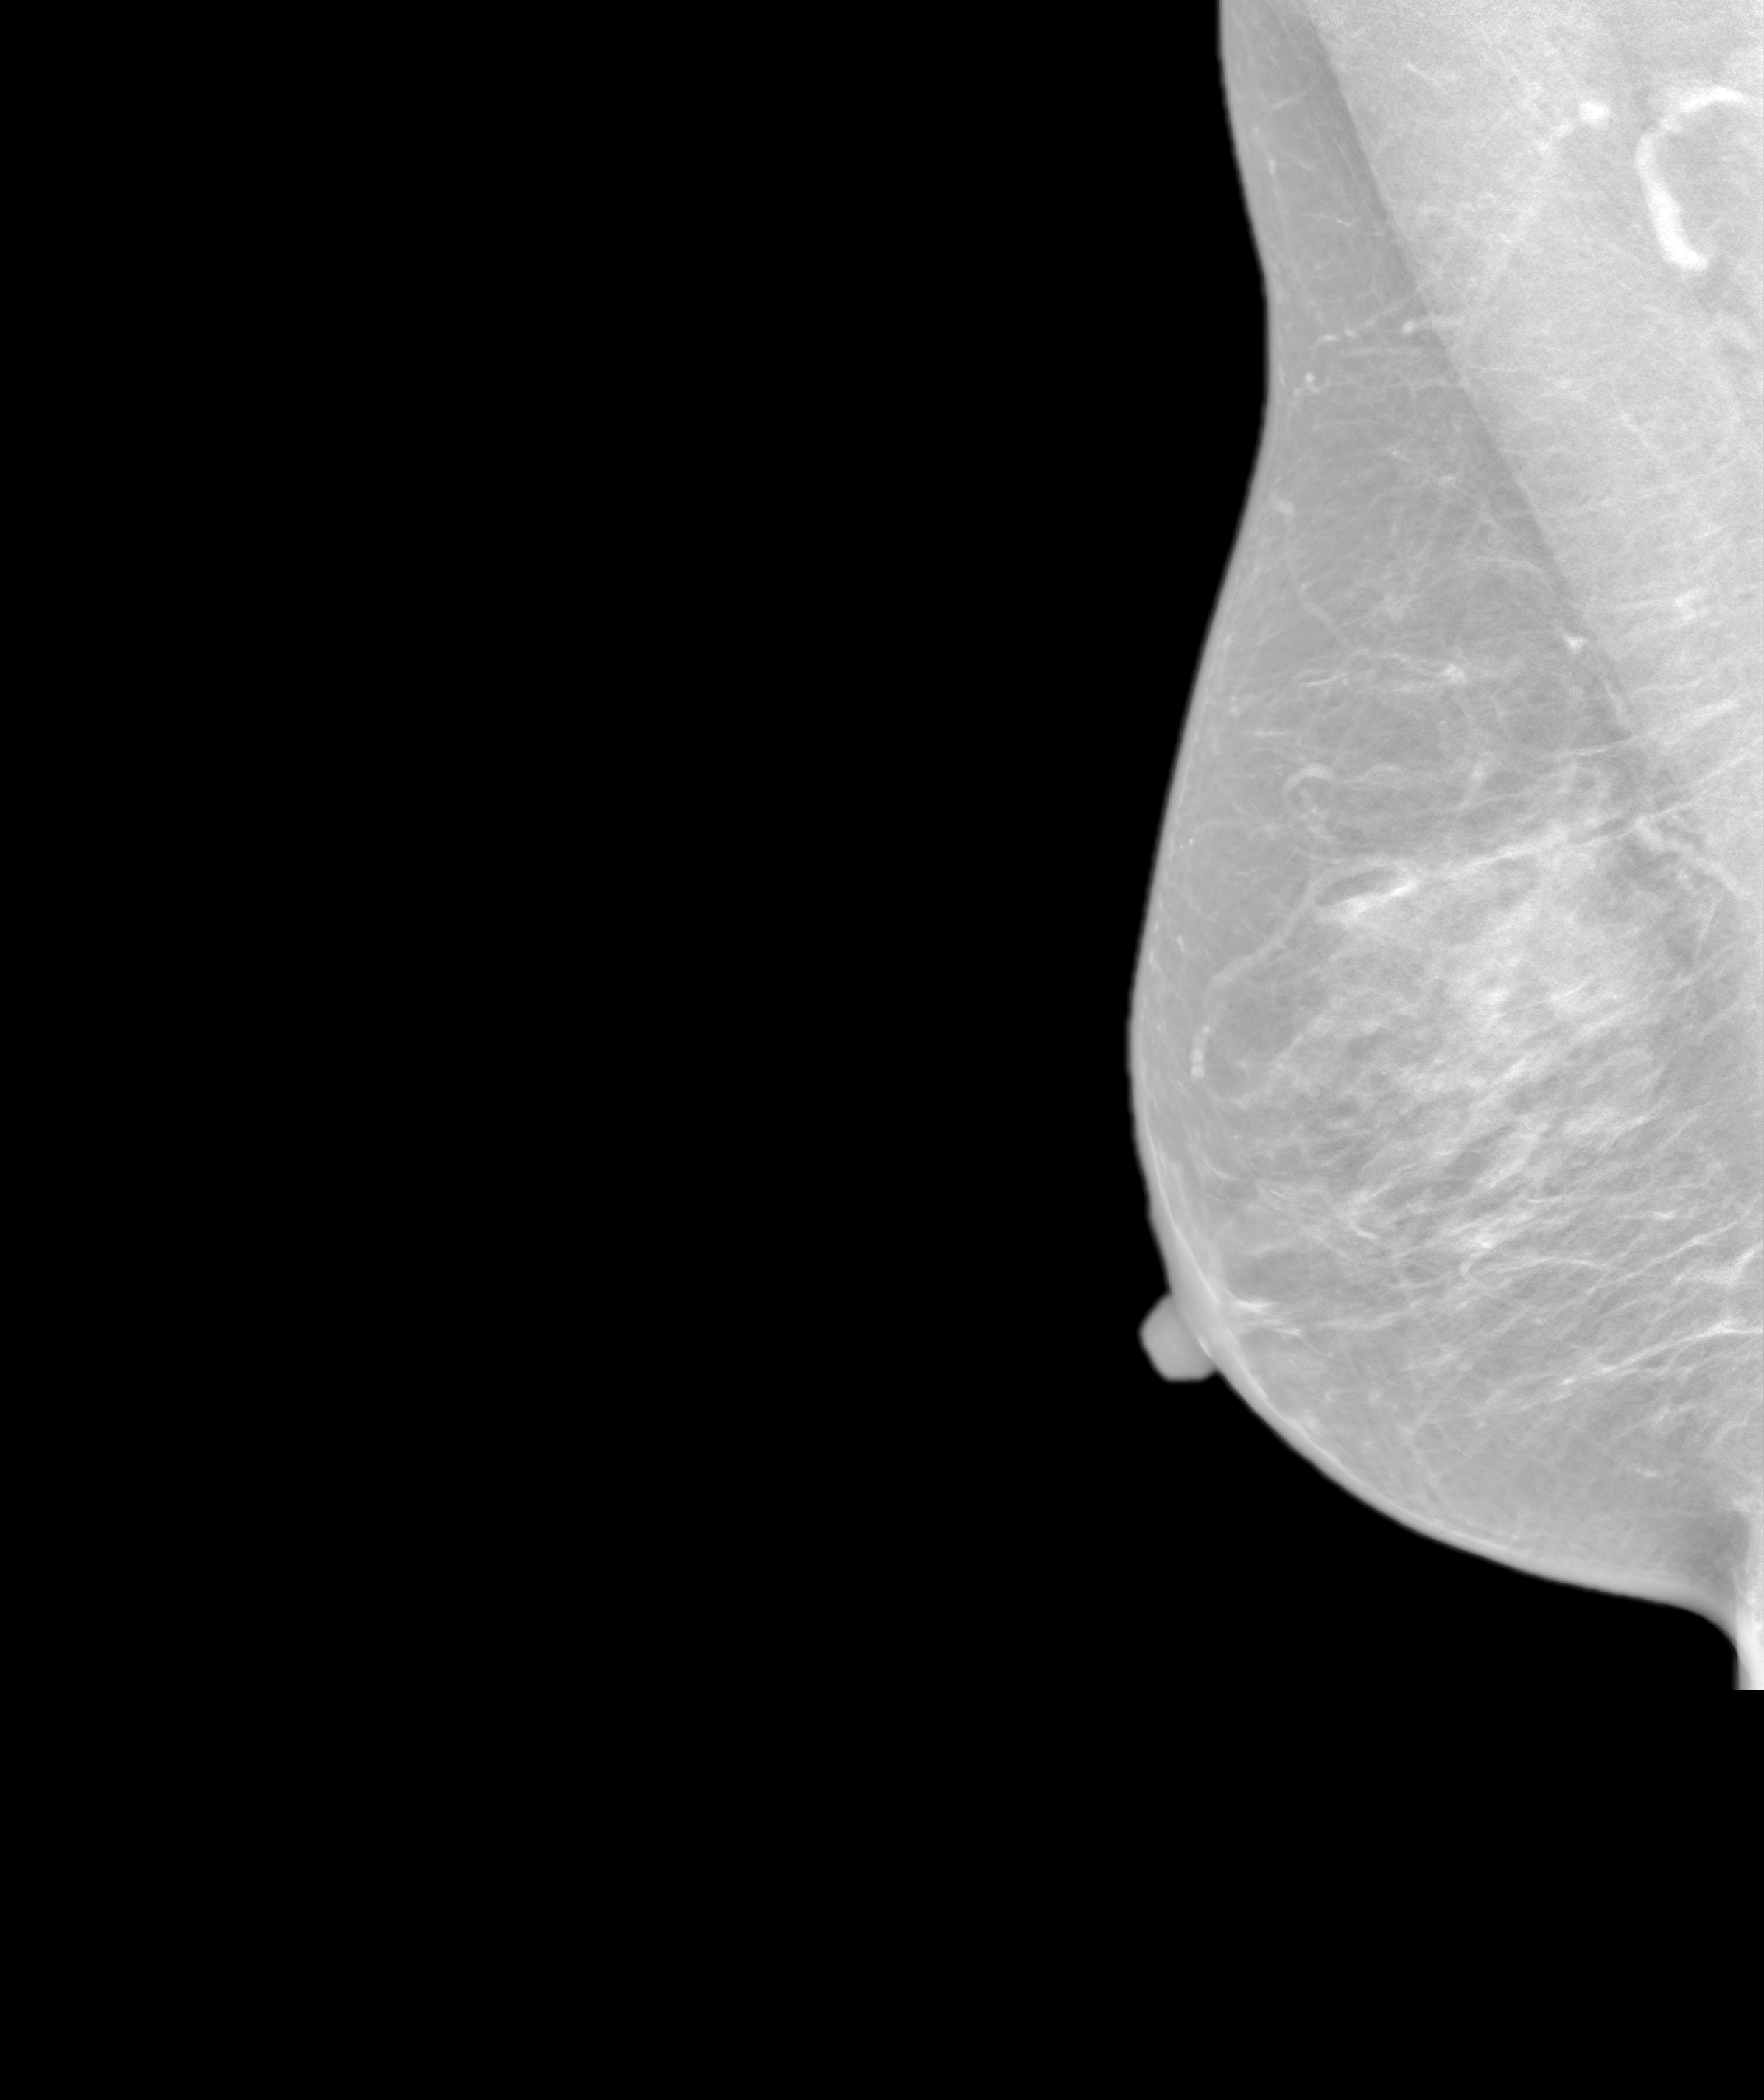
Synthetic 2-D view generated from a tomosynthesis acquisition (not an FFDM exposure), right breast, medio-lateral oblique projection, screening examination, system: SenoIris_1SP1.1(421). Patient aged 48 years (female).
BI-RADS breast density category at the screening exam (both breasts, scale 1–4): 3. Final BI-RADS assessment for this screening round (tomosynthesis exam, both breasts): category 1. Recall: no recall after this screen.